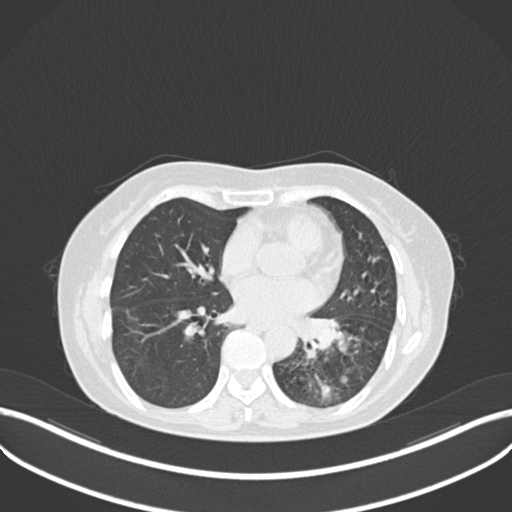
Chest CT, one axial slice. Slice 116 of 270 in the series (ordered by position). Reconstruction kernel B30f. Lung window (W 1500 / L -600 HU). 1 mm slice thickness. 512 × 512 image matrix, field of view 400 × 400 mm. Patient: female, 63 years. Case-level facts recorded for this patient, not image findings: clinical TNM (as recorded): T1b N0 M0.
Outlined on this slice (bounding box drawn by a radiologist):
- lung tumour (recorded histology: adenocarcinoma): bounding box <292,311,344,363> (left, top, right, bottom; pixels)